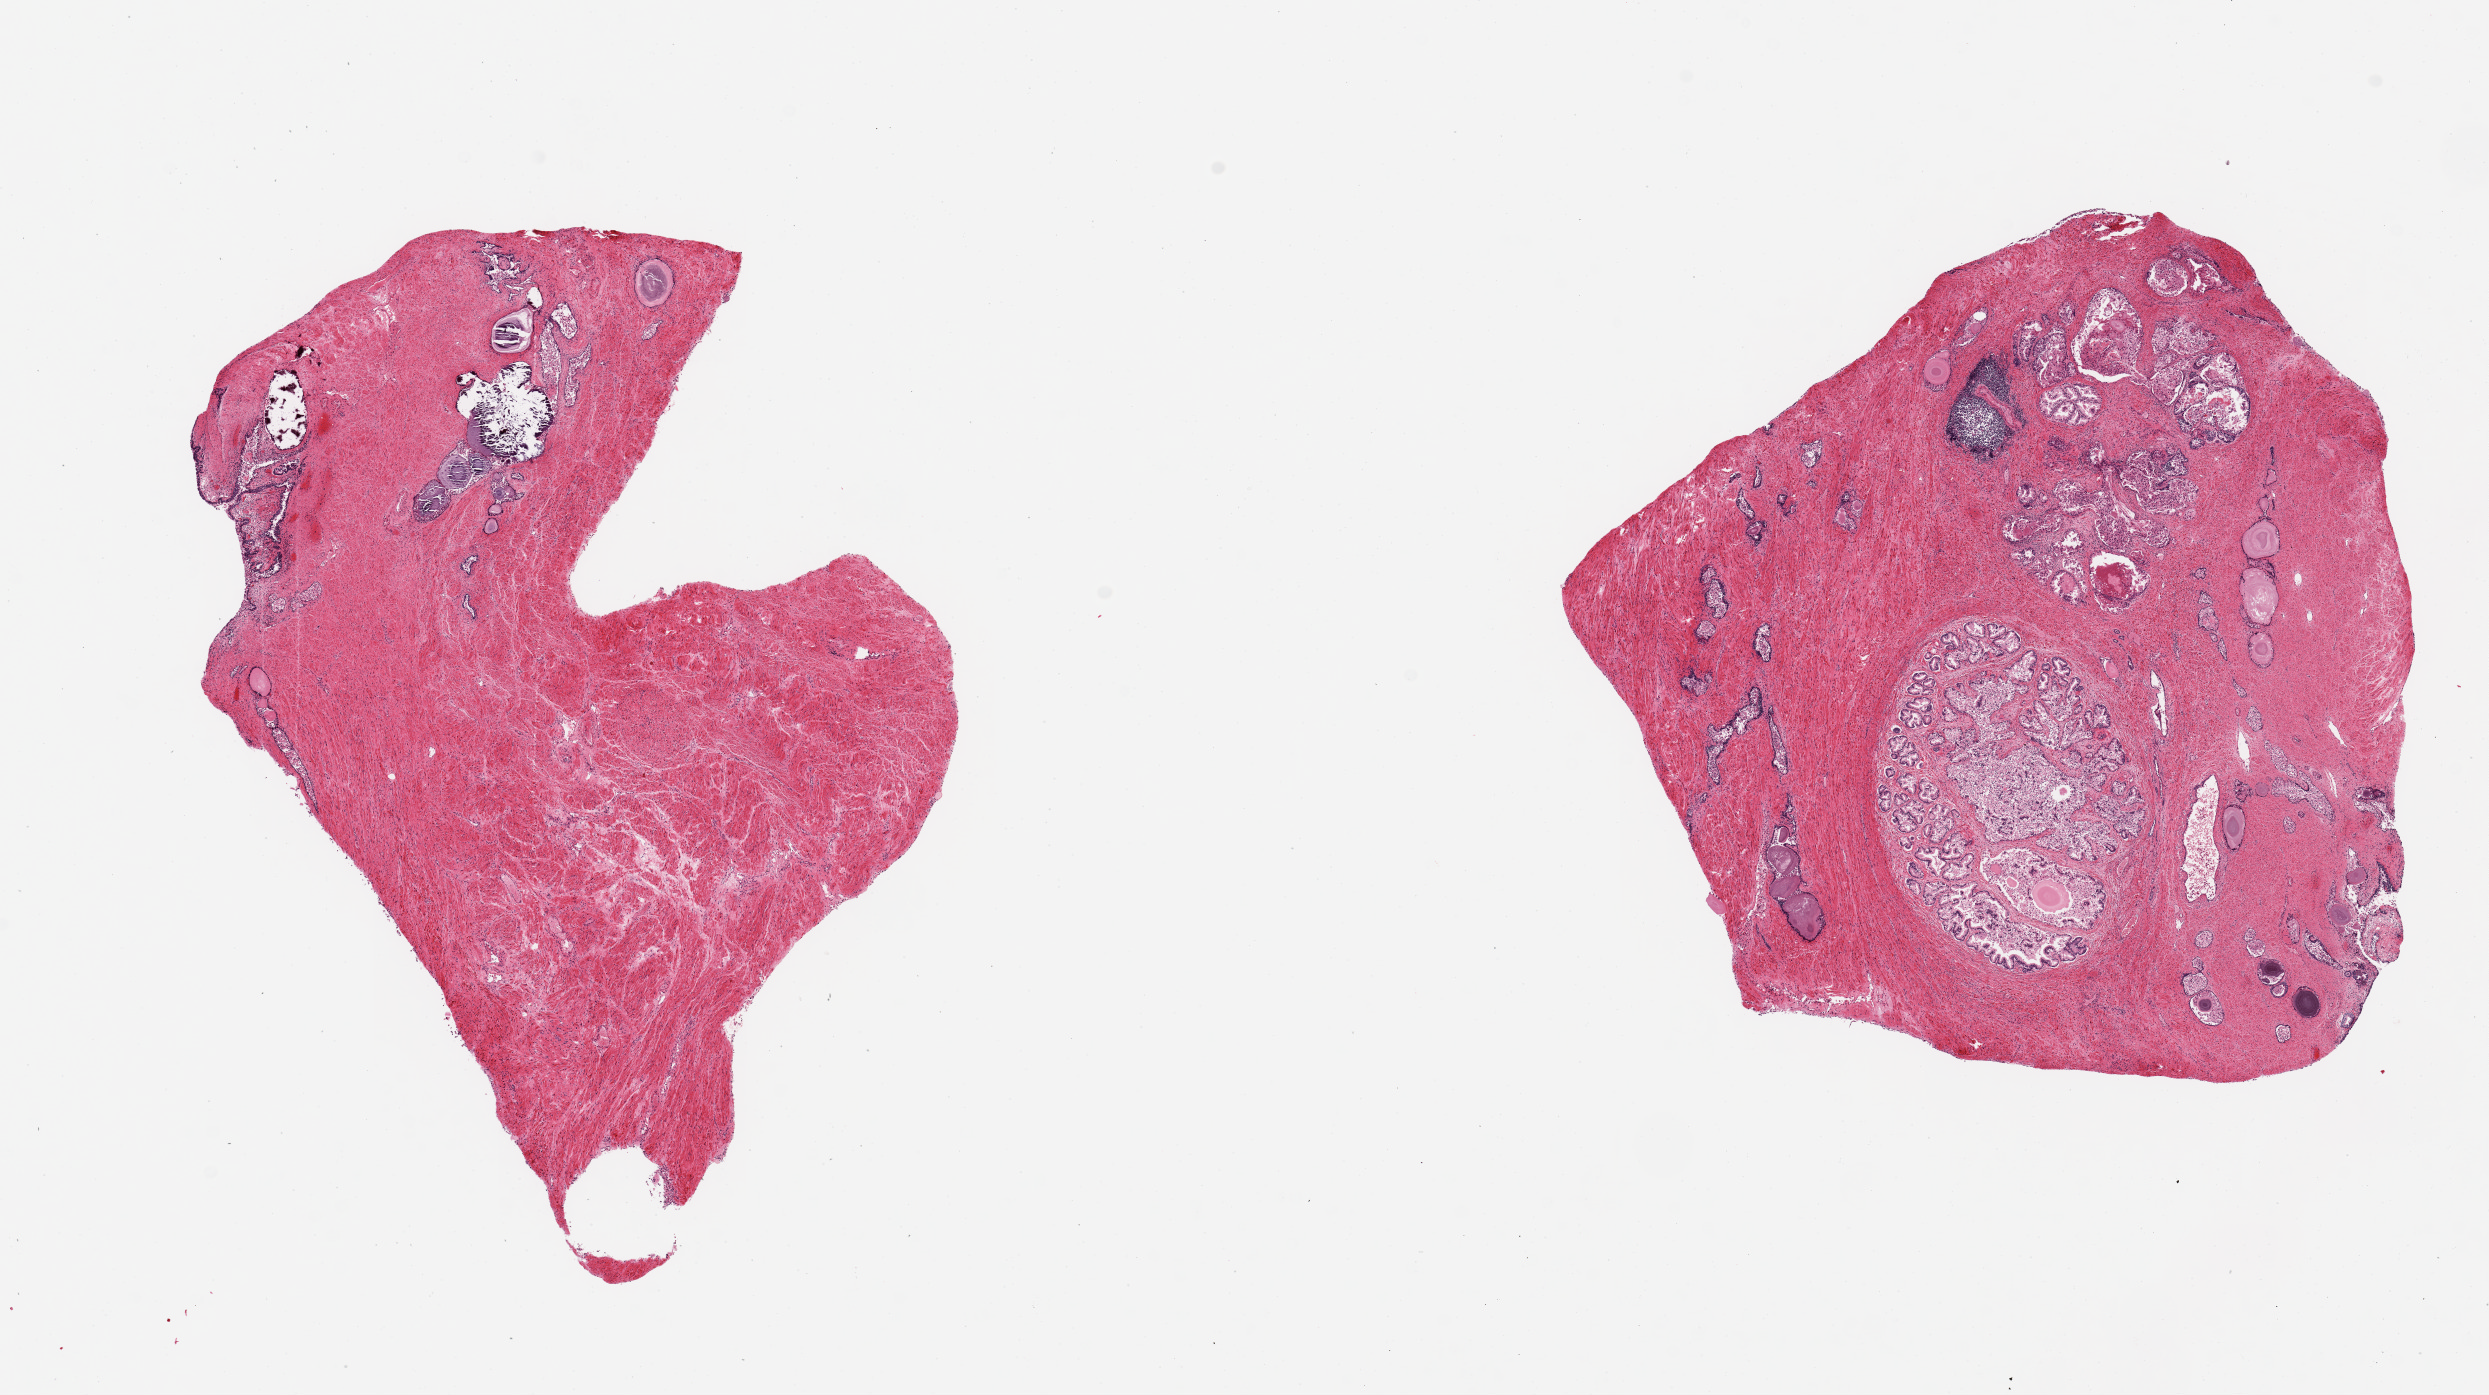
Whole-slide image, haematoxylin and eosin stain — a low-resolution overview of the entire scanned area, about 19.7 x 11.0 mm. PAXgene-fixed paraffin-embedded (PFPE) section. Target tissue: prostate. Tissue donor sample.
Review note (as recorded): 2 pieces ~7x5mm. Glandular elements poorly preserved, glandular and stromal hyperplasia is evident.